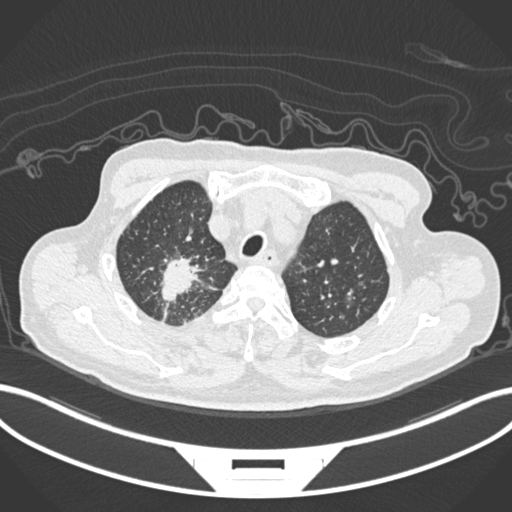
Chest CT, one axial slice; position 177 of 207 along the scan axis; 120 kVp; lung window (W 1500 / L -600 HU); 512 × 512 image matrix. Patient: male, 69 years. From the clinical record (not read from this slice): clinical TNM (as recorded): T1c N1 M1.
Structures marked on this image (rectangle marked by the reading radiologist):
- lung tumour (recorded histology: adenocarcinoma): box from (x=157, y=249) to (x=212, y=315) px